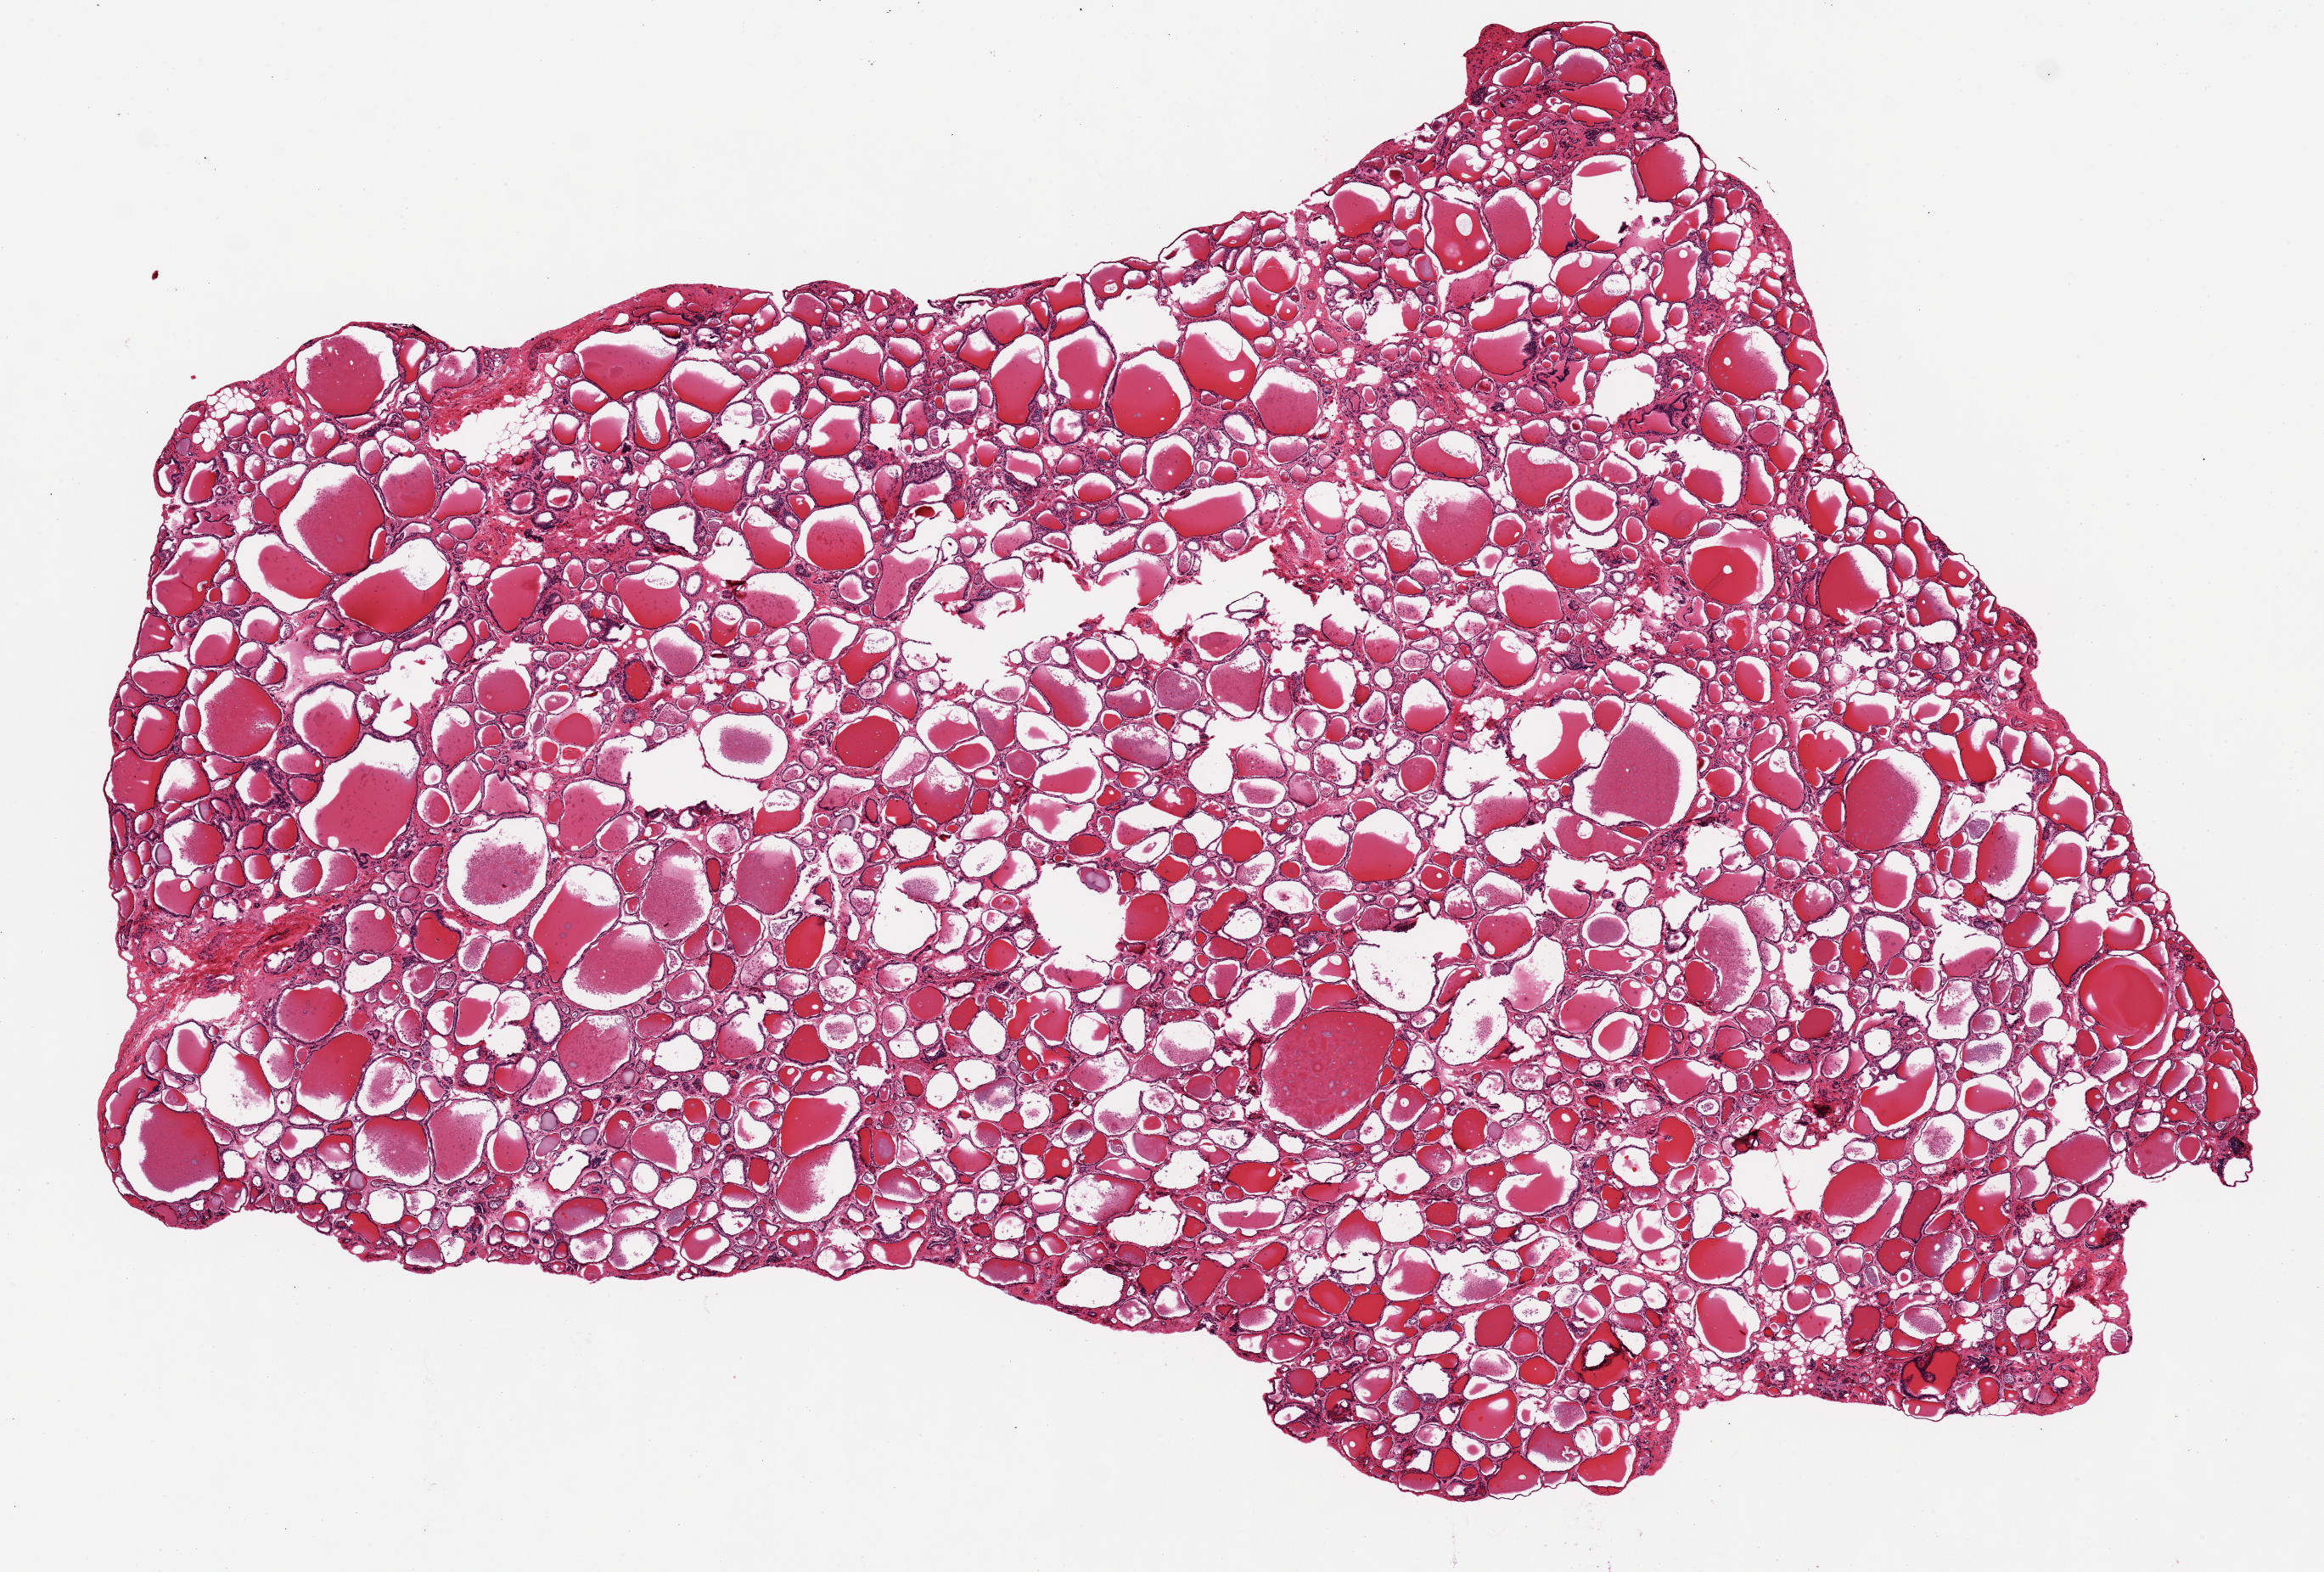
H&E whole-slide image — a low-resolution overview of the entire scanned area, about 10.8 x 7.3 mm, PAXgene-fixed paraffin-embedded (PFPE) section, sampled site (target tissue): thyroid, donor tissue sample. Male donor.
* review note (as recorded): 9.4x6.7. no lesion